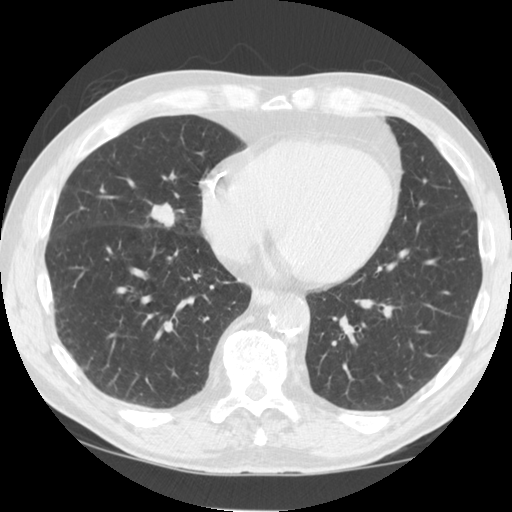
Axial slice from a low-dose chest CT screening exam, third annual screen, lung window (W 1500 / L -600 HU), 2.5 mm slice thickness, standard (soft-tissue) reconstruction kernel (STANDARD), slice 86 of 125 in the series. Male participant, aged 64 years at enrolment. Current smoker at enrolment.
• Lesion marked by an expert reader, box from (x=130, y=188) to (x=204, y=242) px.
• Reader record for this screening exam (exam-level; its link to the box is not recorded): non-calcified nodule or mass ≥4 mm, right middle lobe, 21 × 14 mm, smooth margins, soft tissue attenuation, pre-existing on the prior screen: yes; interval growth: yes.
• Later outcome: lung cancer diagnosed 74 days after this screen — non-small cell carcinoma, right middle lobe, poorly differentiated (G3), stage IIIA (AJCC 6th edition), 20 mm at pathology.